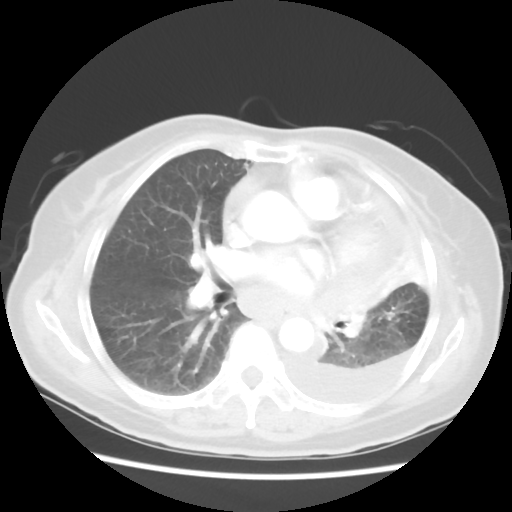
Chest CT, one axial slice; reconstruction kernel STANDARD; 120 kVp; lung window (W 1500 / L -600 HU); 5 mm slice thickness; 512 × 512 image matrix. Female patient, age 72 years. From the clinical record (not read from this slice): clinical TNM (as recorded): T4 N3 M1b; histopathological grade: G3.
Outlined on this slice (rectangle marked by the reading radiologist):
- lung tumour (recorded histology: large cell carcinoma): bounding box [x1, y1, x2, y2] px = [314, 280, 384, 341]